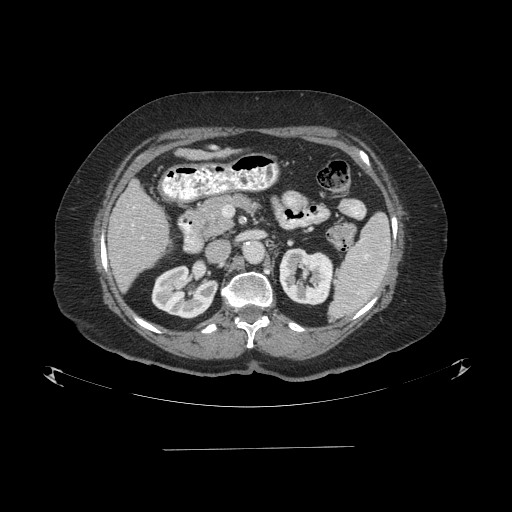
Contrast-enhanced abdominal CT (liver protocol), one axial slice. Slice 38 of 103 in the series (ordered by position). Reconstruction kernel STANDARD. 120 kVp. One of 2 acquisitions stored at this slice position. Soft-tissue window (W 400 / L 40 HU). 2.5 mm slice thickness. 512 × 512 image matrix, field of view 500 × 500 mm. Case-level facts recorded for this patient, not image findings: diagnosis: hepatocellular carcinoma (patient treated with transarterial chemoembolisation; whether this scan precedes or follows treatment is not stated here); TNM stage (as recorded): Stage-IIIA; Child-Pugh class: A; tumour nodularity: multinodular.
Structures marked on this image (semi-automatic segmentation, software-assisted and operator-edited):
- liver parenchyma outside the tumour (the mass and vessels are separate outlines, so this box may not span the whole liver): bounding box (x1, y1, x2, y2) in pixels: (108, 178, 168, 290)
- liver vessels: (142, 237, 144, 239)